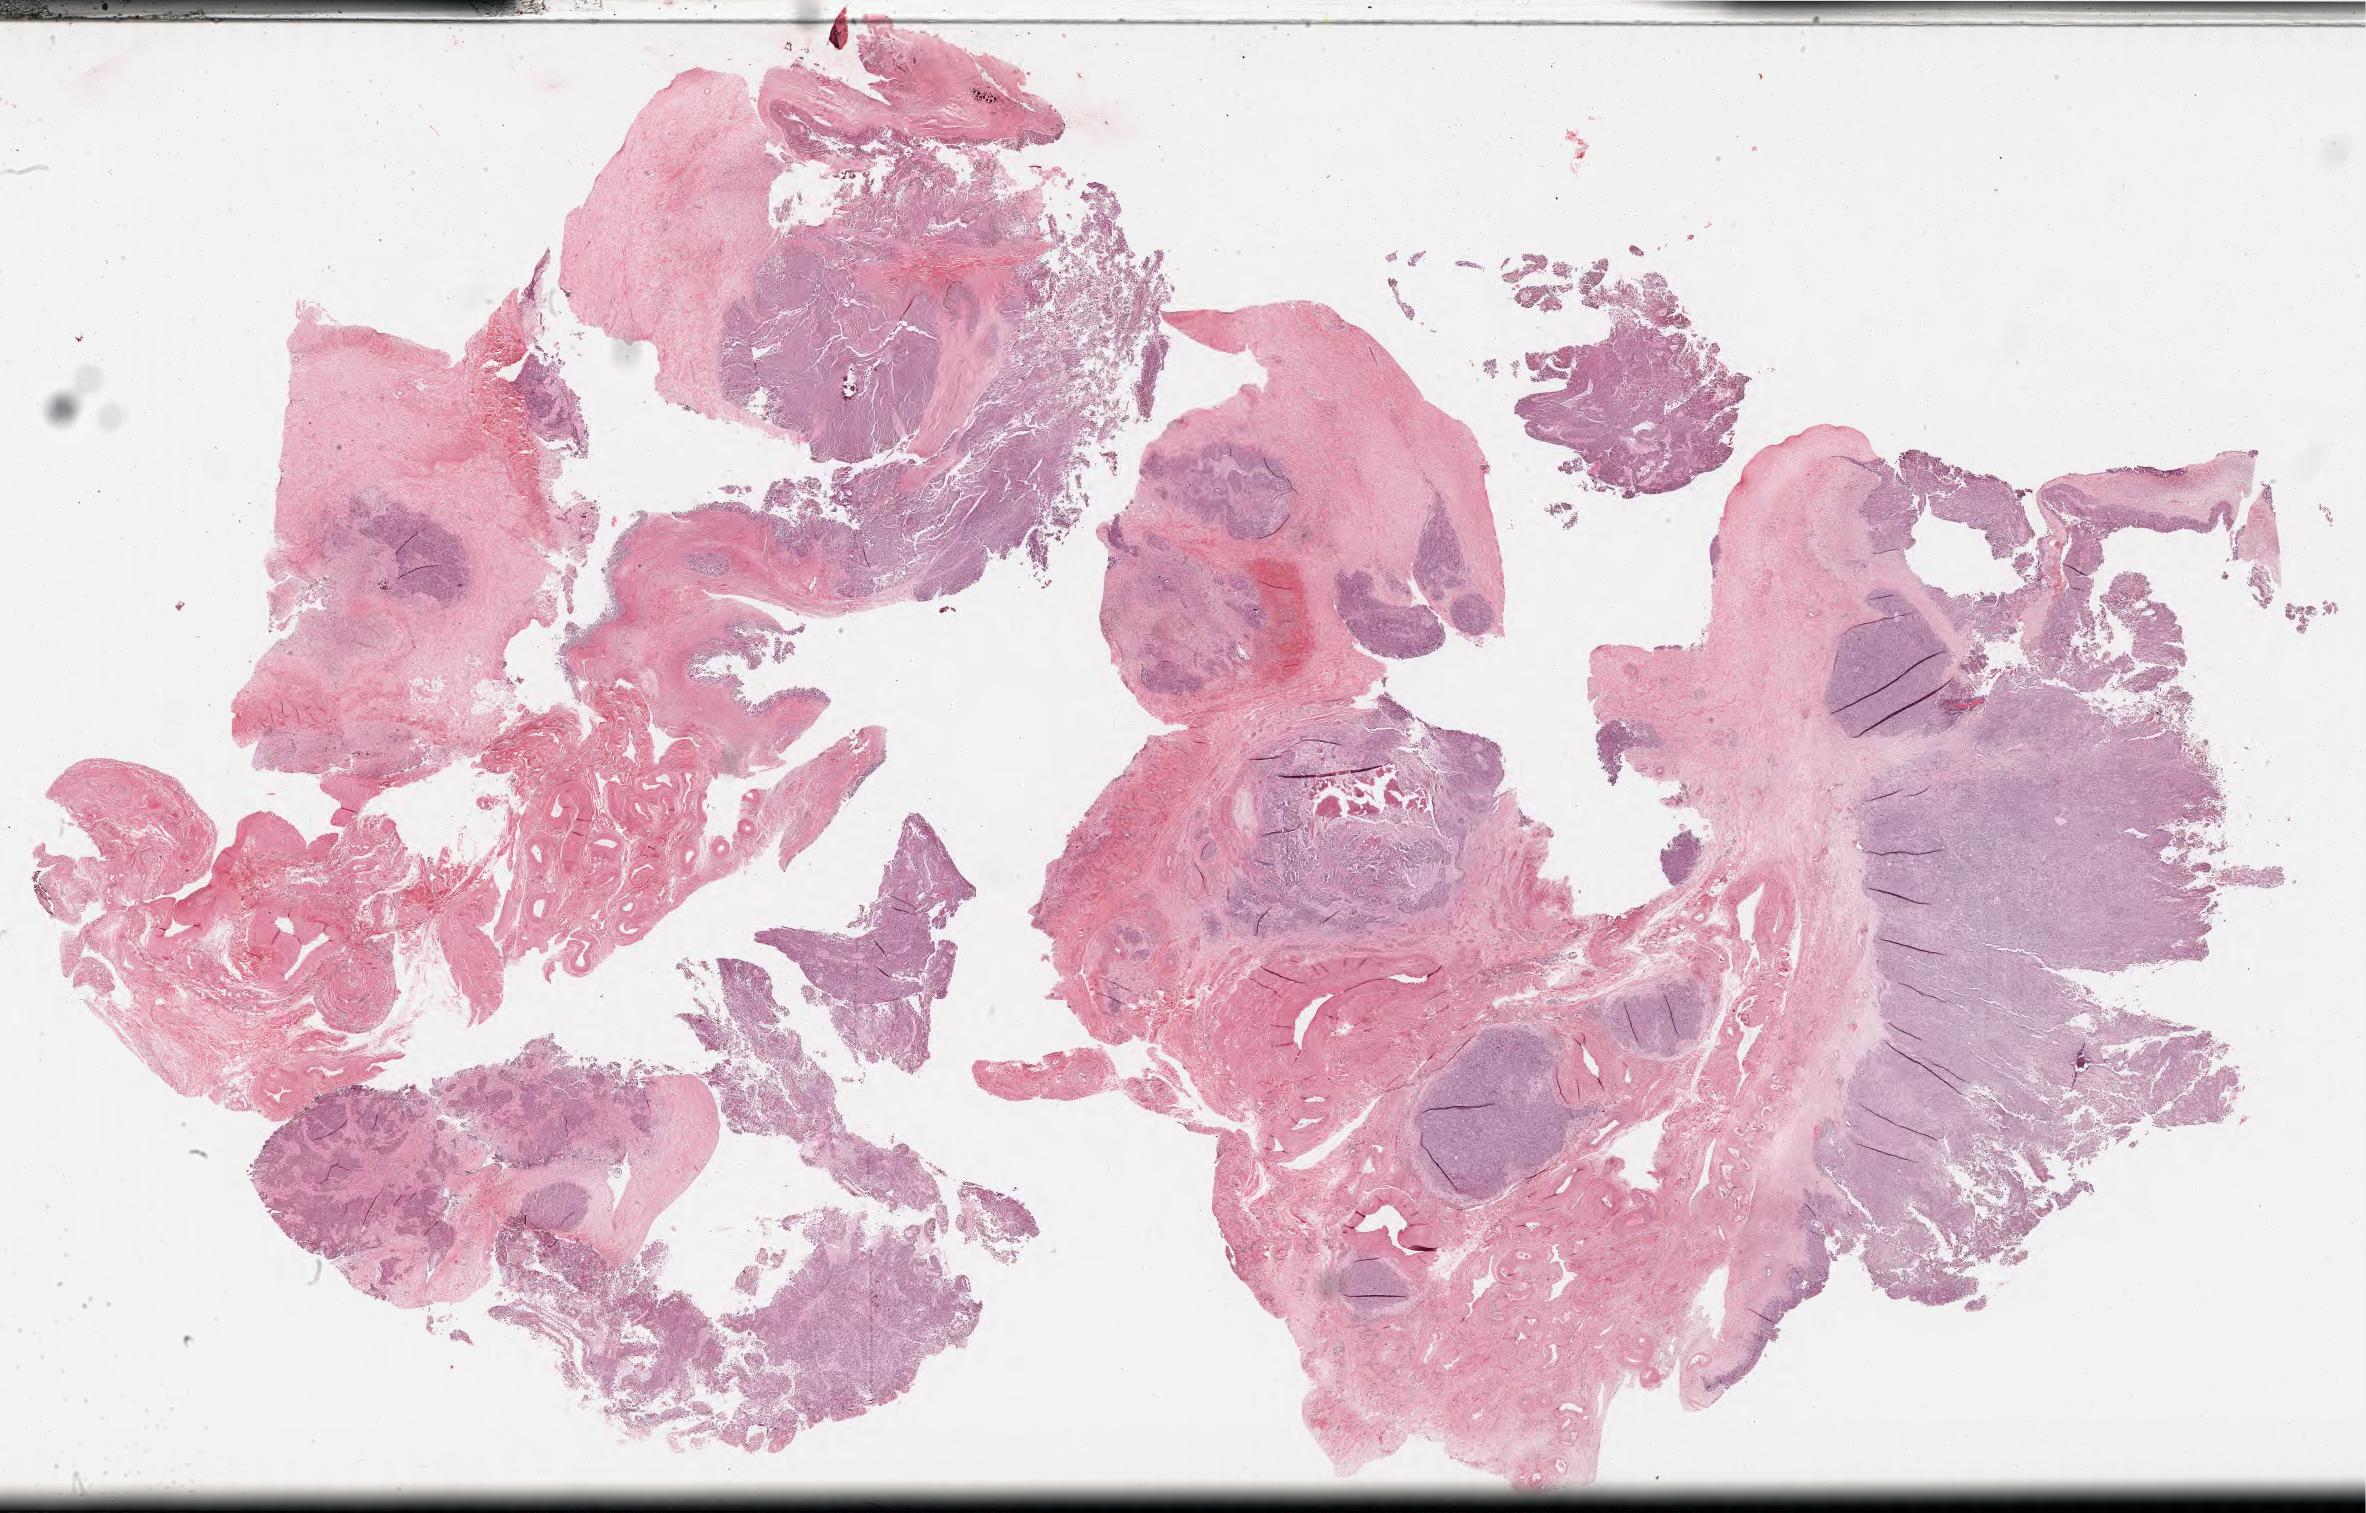
H&E-stained whole-slide image — shown as a low-resolution overview of the whole scanned area (about 38.2 x 24.4 mm, acquisition: 40x scan), formalin-fixed paraffin-embedded (FFPE) diagnostic section, sample: primary tumour, ovary. Female, age 73 years at initial diagnosis.
Pathologic diagnosis: Serous cystadenocarcinoma, NOS.